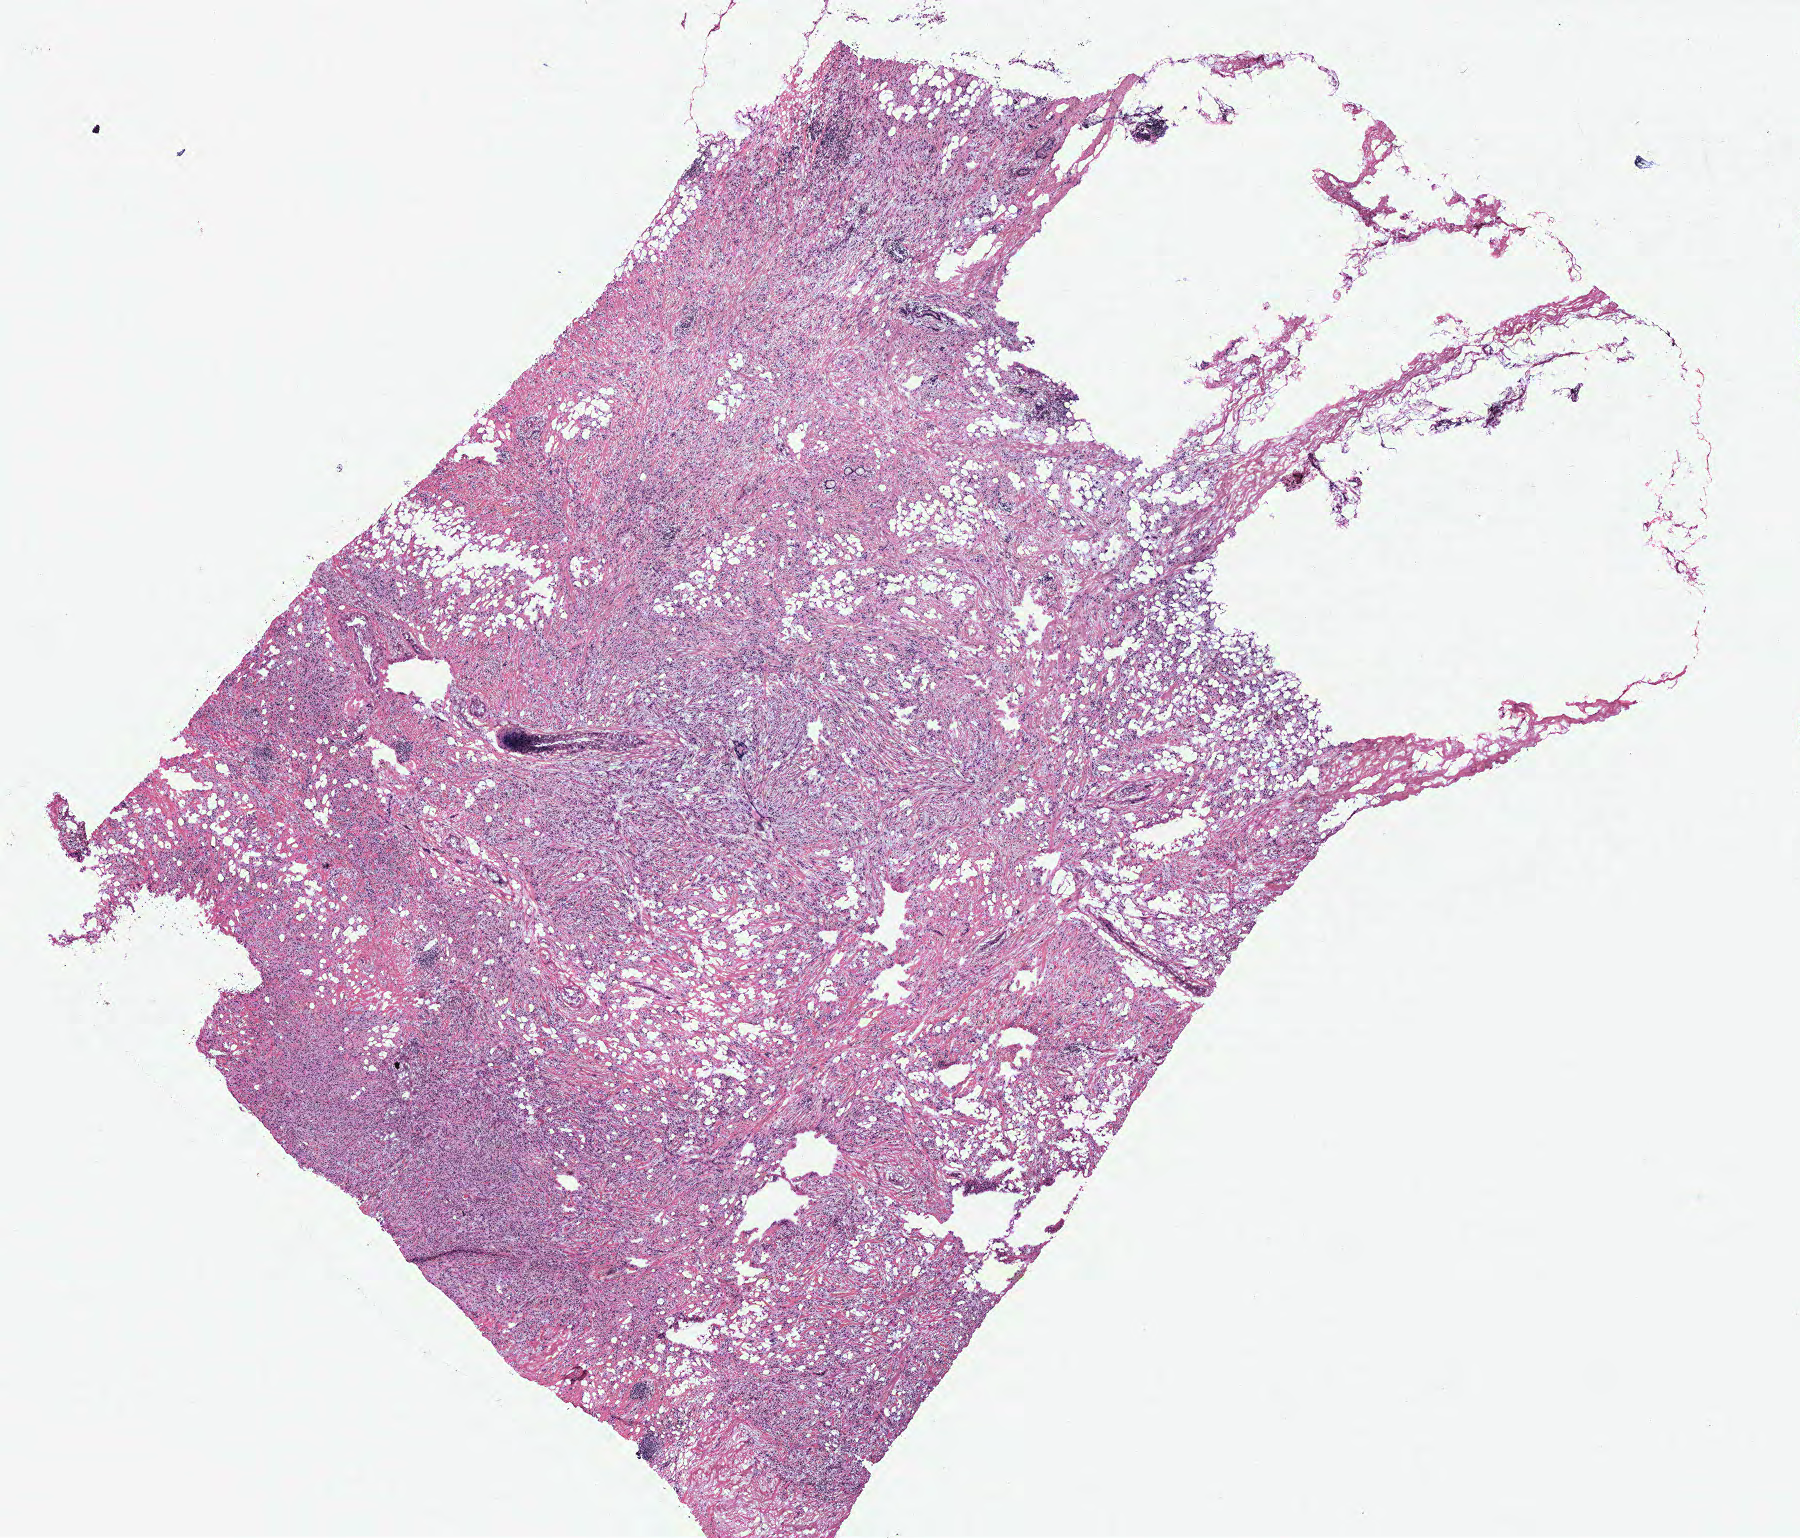
Whole-slide histology image, H&E-stained, whole scanned area (about 14.4 x 12.3 mm) shown as a low-resolution overview, breast, tissue type not recorded. Female patient.
Patient diagnosis: Infiltrating duct carcinoma, NOS.